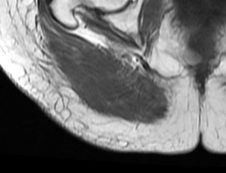
MRI of an extremity soft-tissue mass, one axial slice; slice 25 of 73 in the series (ordered by position); MR volume resampled by the dataset authors to the PET/CT grid (not the native acquisition matrix); 226 × 173 image matrix. Female patient. From the clinical record (not read from this slice): histological type: spindle cell suggestive of myxofibrosarcoma; grade: intermediate; site of the primary tumour: right buttock.
Annotated regions visible in this slice (expert contour drawn on MRI and transferred to this co-registered scan by the dataset authors):
- gross tumour volume (mass): bounding box (x1, y1, x2, y2) in pixels: (45, 42, 124, 102)